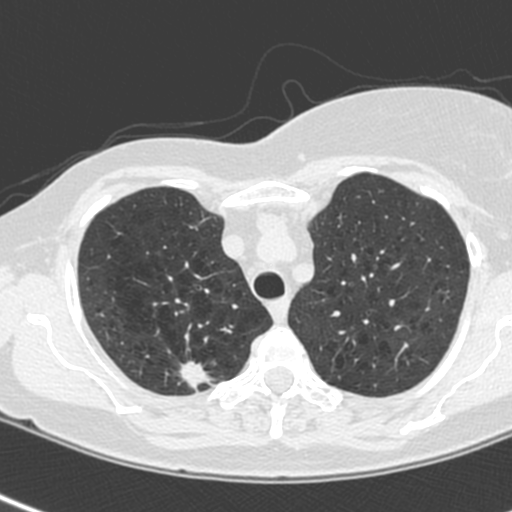
Low-dose screening chest CT, axial slice. First (baseline) screen. Lung window (W 1500 / L -600 HU). 1.3 mm slice thickness. Female participant, aged 64 years at enrolment. Current smoker at enrolment.
Expert reader's lesion annotation, box from (x=166, y=354) to (x=221, y=404) px. The exam's reader record, not a measurement of the box and not confirmed to be the same lesion: non-calcified nodule or mass ≥4 mm, right upper lobe, 13 × 10 mm, spiculated (stellate) margins, soft tissue attenuation. Official screen result: positive, change unspecified: nodule(s) >= 4 mm or enlarging nodule(s), mass(es), or other non-specific abnormalities suspicious for lung cancer. Lung cancer was diagnosed 21 days after this screen: adenocarcinoma, NOS, right upper lobe, poorly differentiated (G3), stage IIIB (AJCC 6th edition), 20 mm at pathology.